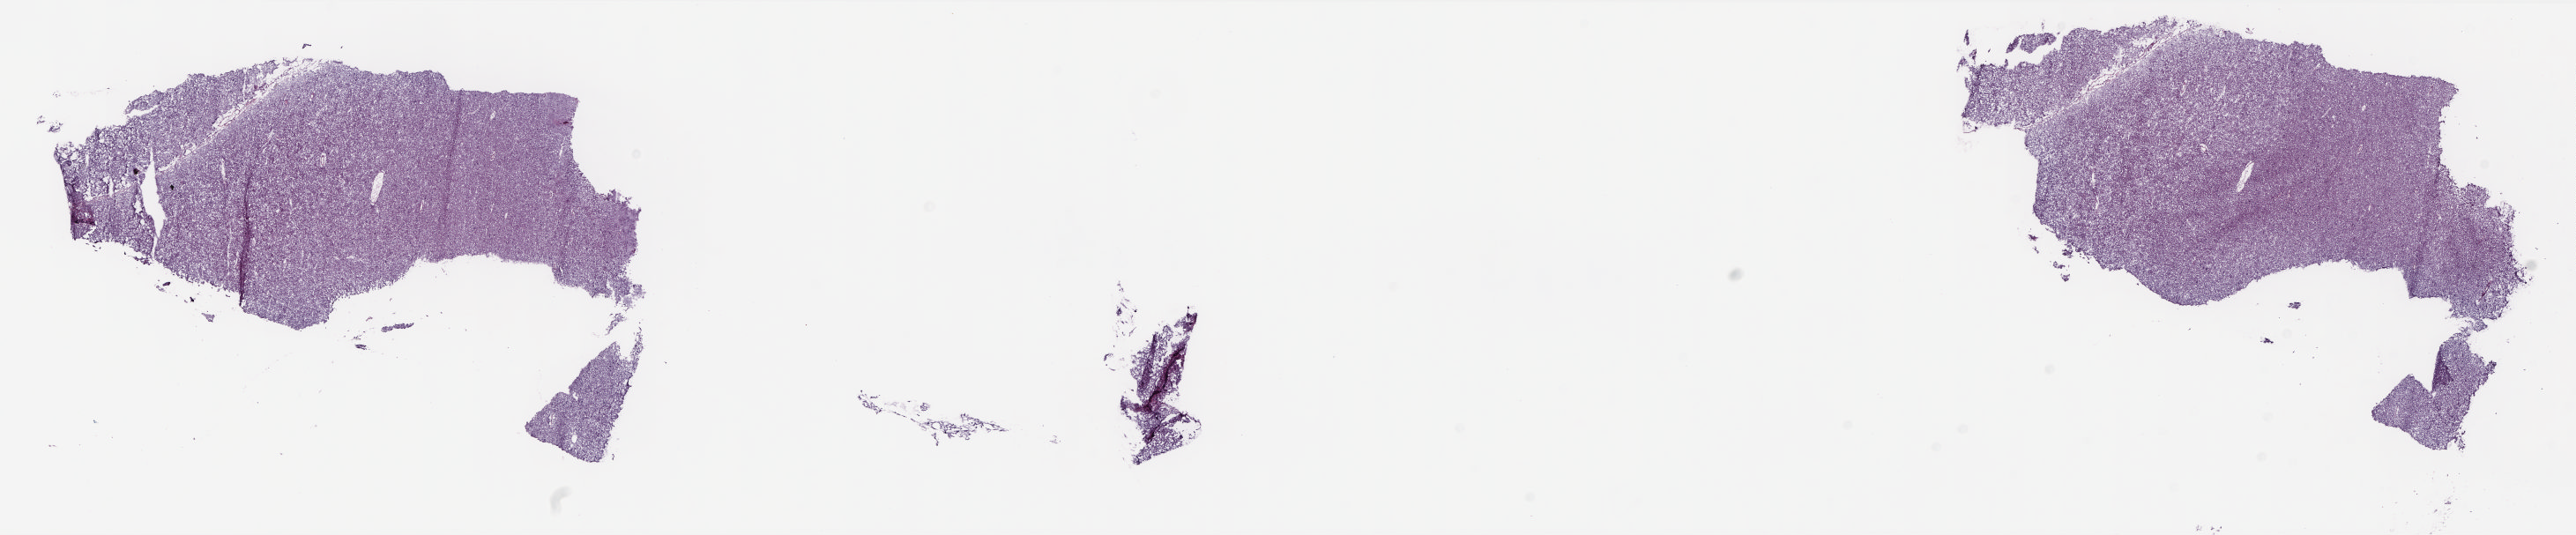
Hematoxylin and eosin (H&E) stained whole-slide image — whole scanned area (about 23.6 x 4.9 mm, from a 20x scan) shown as a low-resolution overview; frozen section from the top of the tissue portion; brain, solid tissue normal (non-tumour tissue) sample. Composition of this section per pathologist review: tumour cells 0%, tumour nuclei 0%, normal cells 25%, stromal cells 75%, necrosis 0%. Infiltration values recorded for this section: lymphocyte infiltration 0%, monocyte infiltration 0%, neutrophil infiltration 0%.
This section: solid tissue normal sample (biorepository sample class).